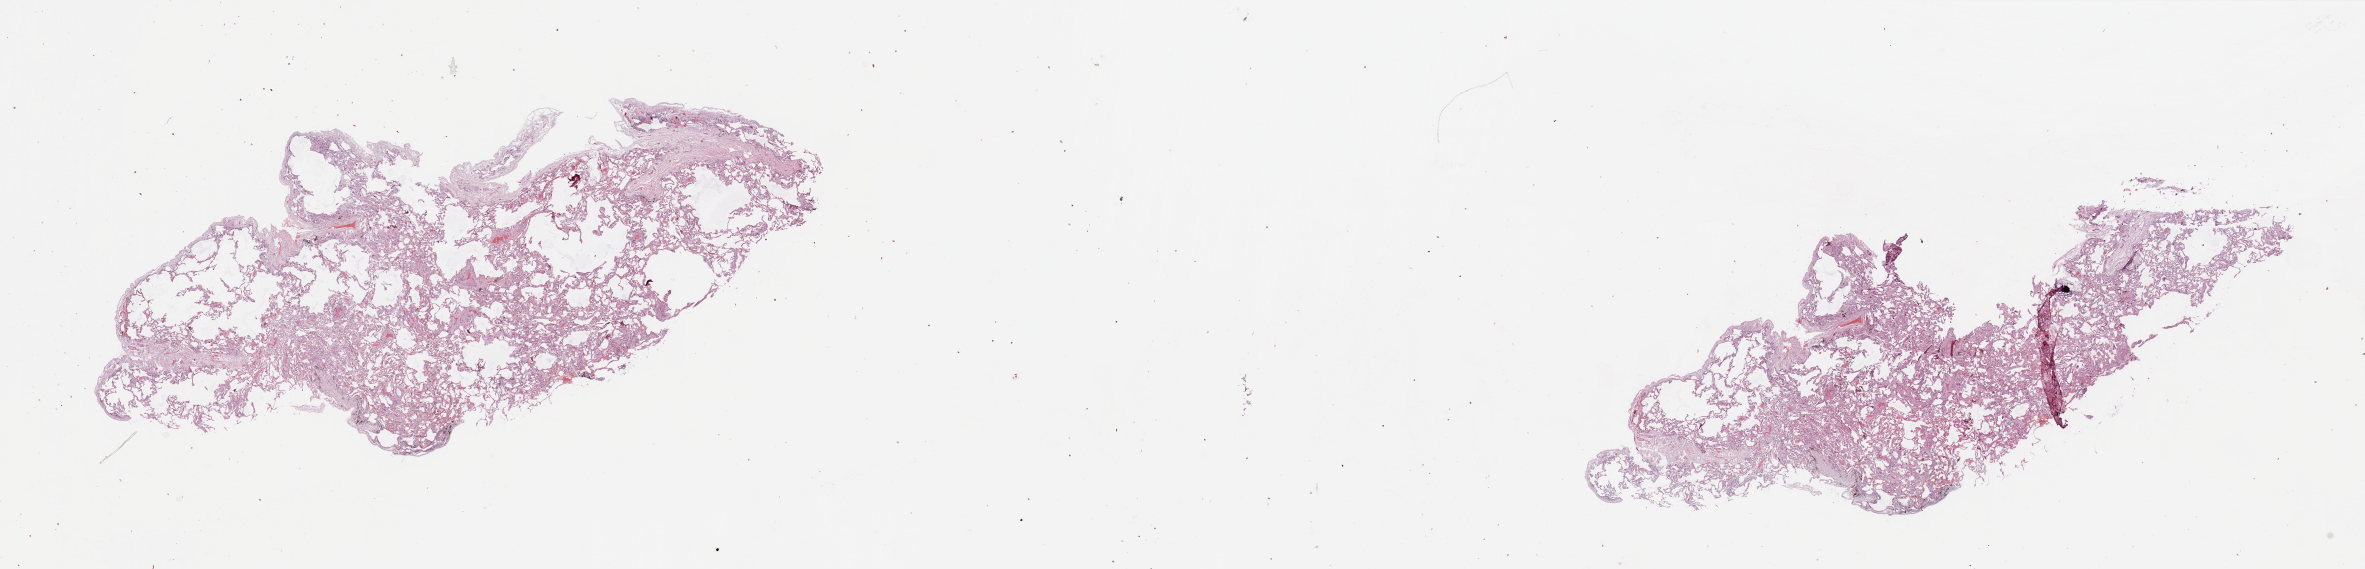
Whole-slide histology image, Hematoxylin and eosin (H&E) stained — a low-resolution overview of the entire scanned area, about 37.4 x 9.0 mm (slide scanned at 20x); normal (non-tumour) tissue sample, sampled site: lung. Patient: male, age 72 years.
This section: normal (non-tumour) tissue from the same patient. Patient diagnosis: Squamous cell carcinoma, NOS.